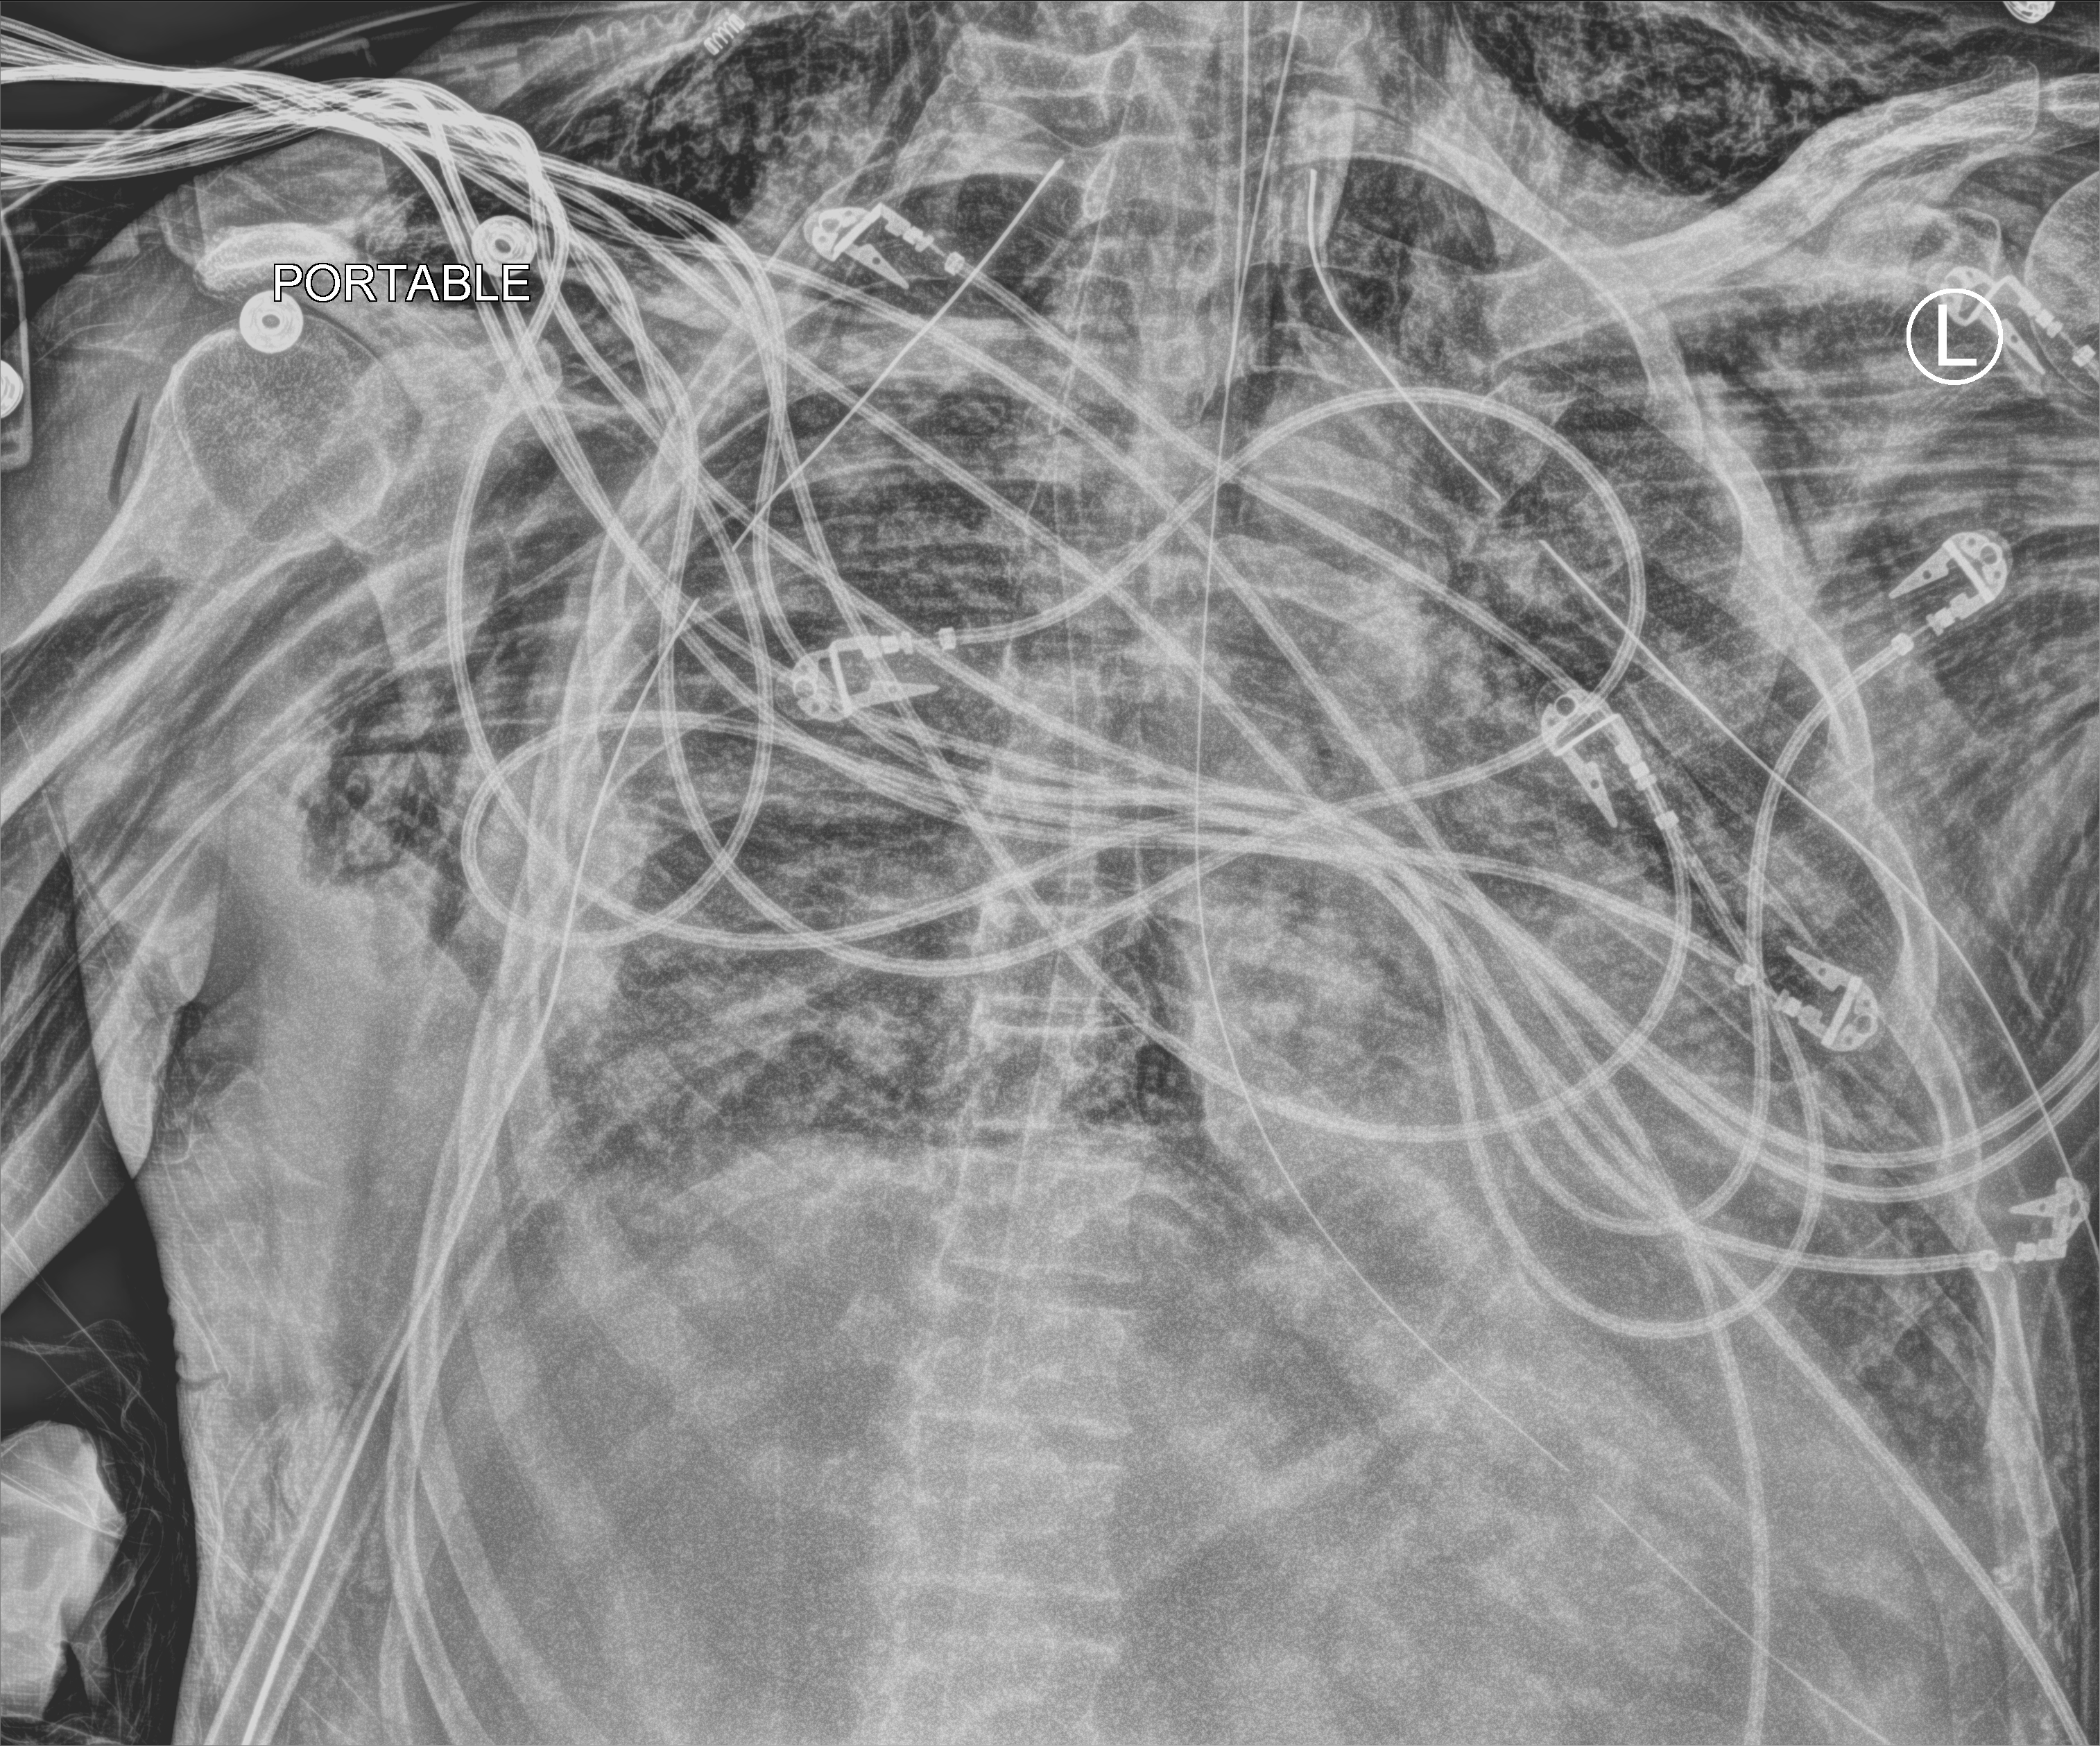
Portable chest radiograph, anteroposterior (AP) projection. Patient hospitalised with COVID-19; male, aged 18–59 years.
From the hospital-stay record, not from the radiograph (when in the stay this image was taken is not recorded): admitted to intensive care during this hospital stay: yes; length of hospital stay: 83 days.